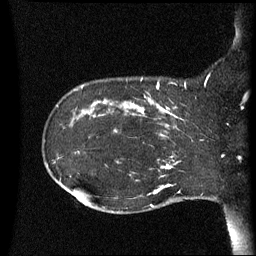
Breast MRI (dynamic contrast-enhanced), one sagittal slice. Position 18 of 60 along the scan axis. Dynamic contrast-enhanced series, image 2 of 3 at this slice position (ordered by acquisition). 1.5 T. TE 4.2 ms, TR 8.4 ms. 2.5 mm slice thickness. 256 × 256 image matrix, field of view 220 × 220 mm. Patient: female, 41 years. From the clinical record (not read from this slice): setting: breast cancer imaged before/during neoadjuvant chemotherapy; receptor status: HER2-positive.
Annotated regions visible in this slice (semi-automatic segmentation, software-assisted and operator-edited):
- analysis volume of interest (the breast-tissue region the enhancement analysis was run in; not a lesion): box from (x=122, y=84) to (x=195, y=137) px
- tumour enhancement mask (voxels above the 70 % enhancement threshold inside the analysis volume of interest): (x=125, y=84)–(x=183, y=137)